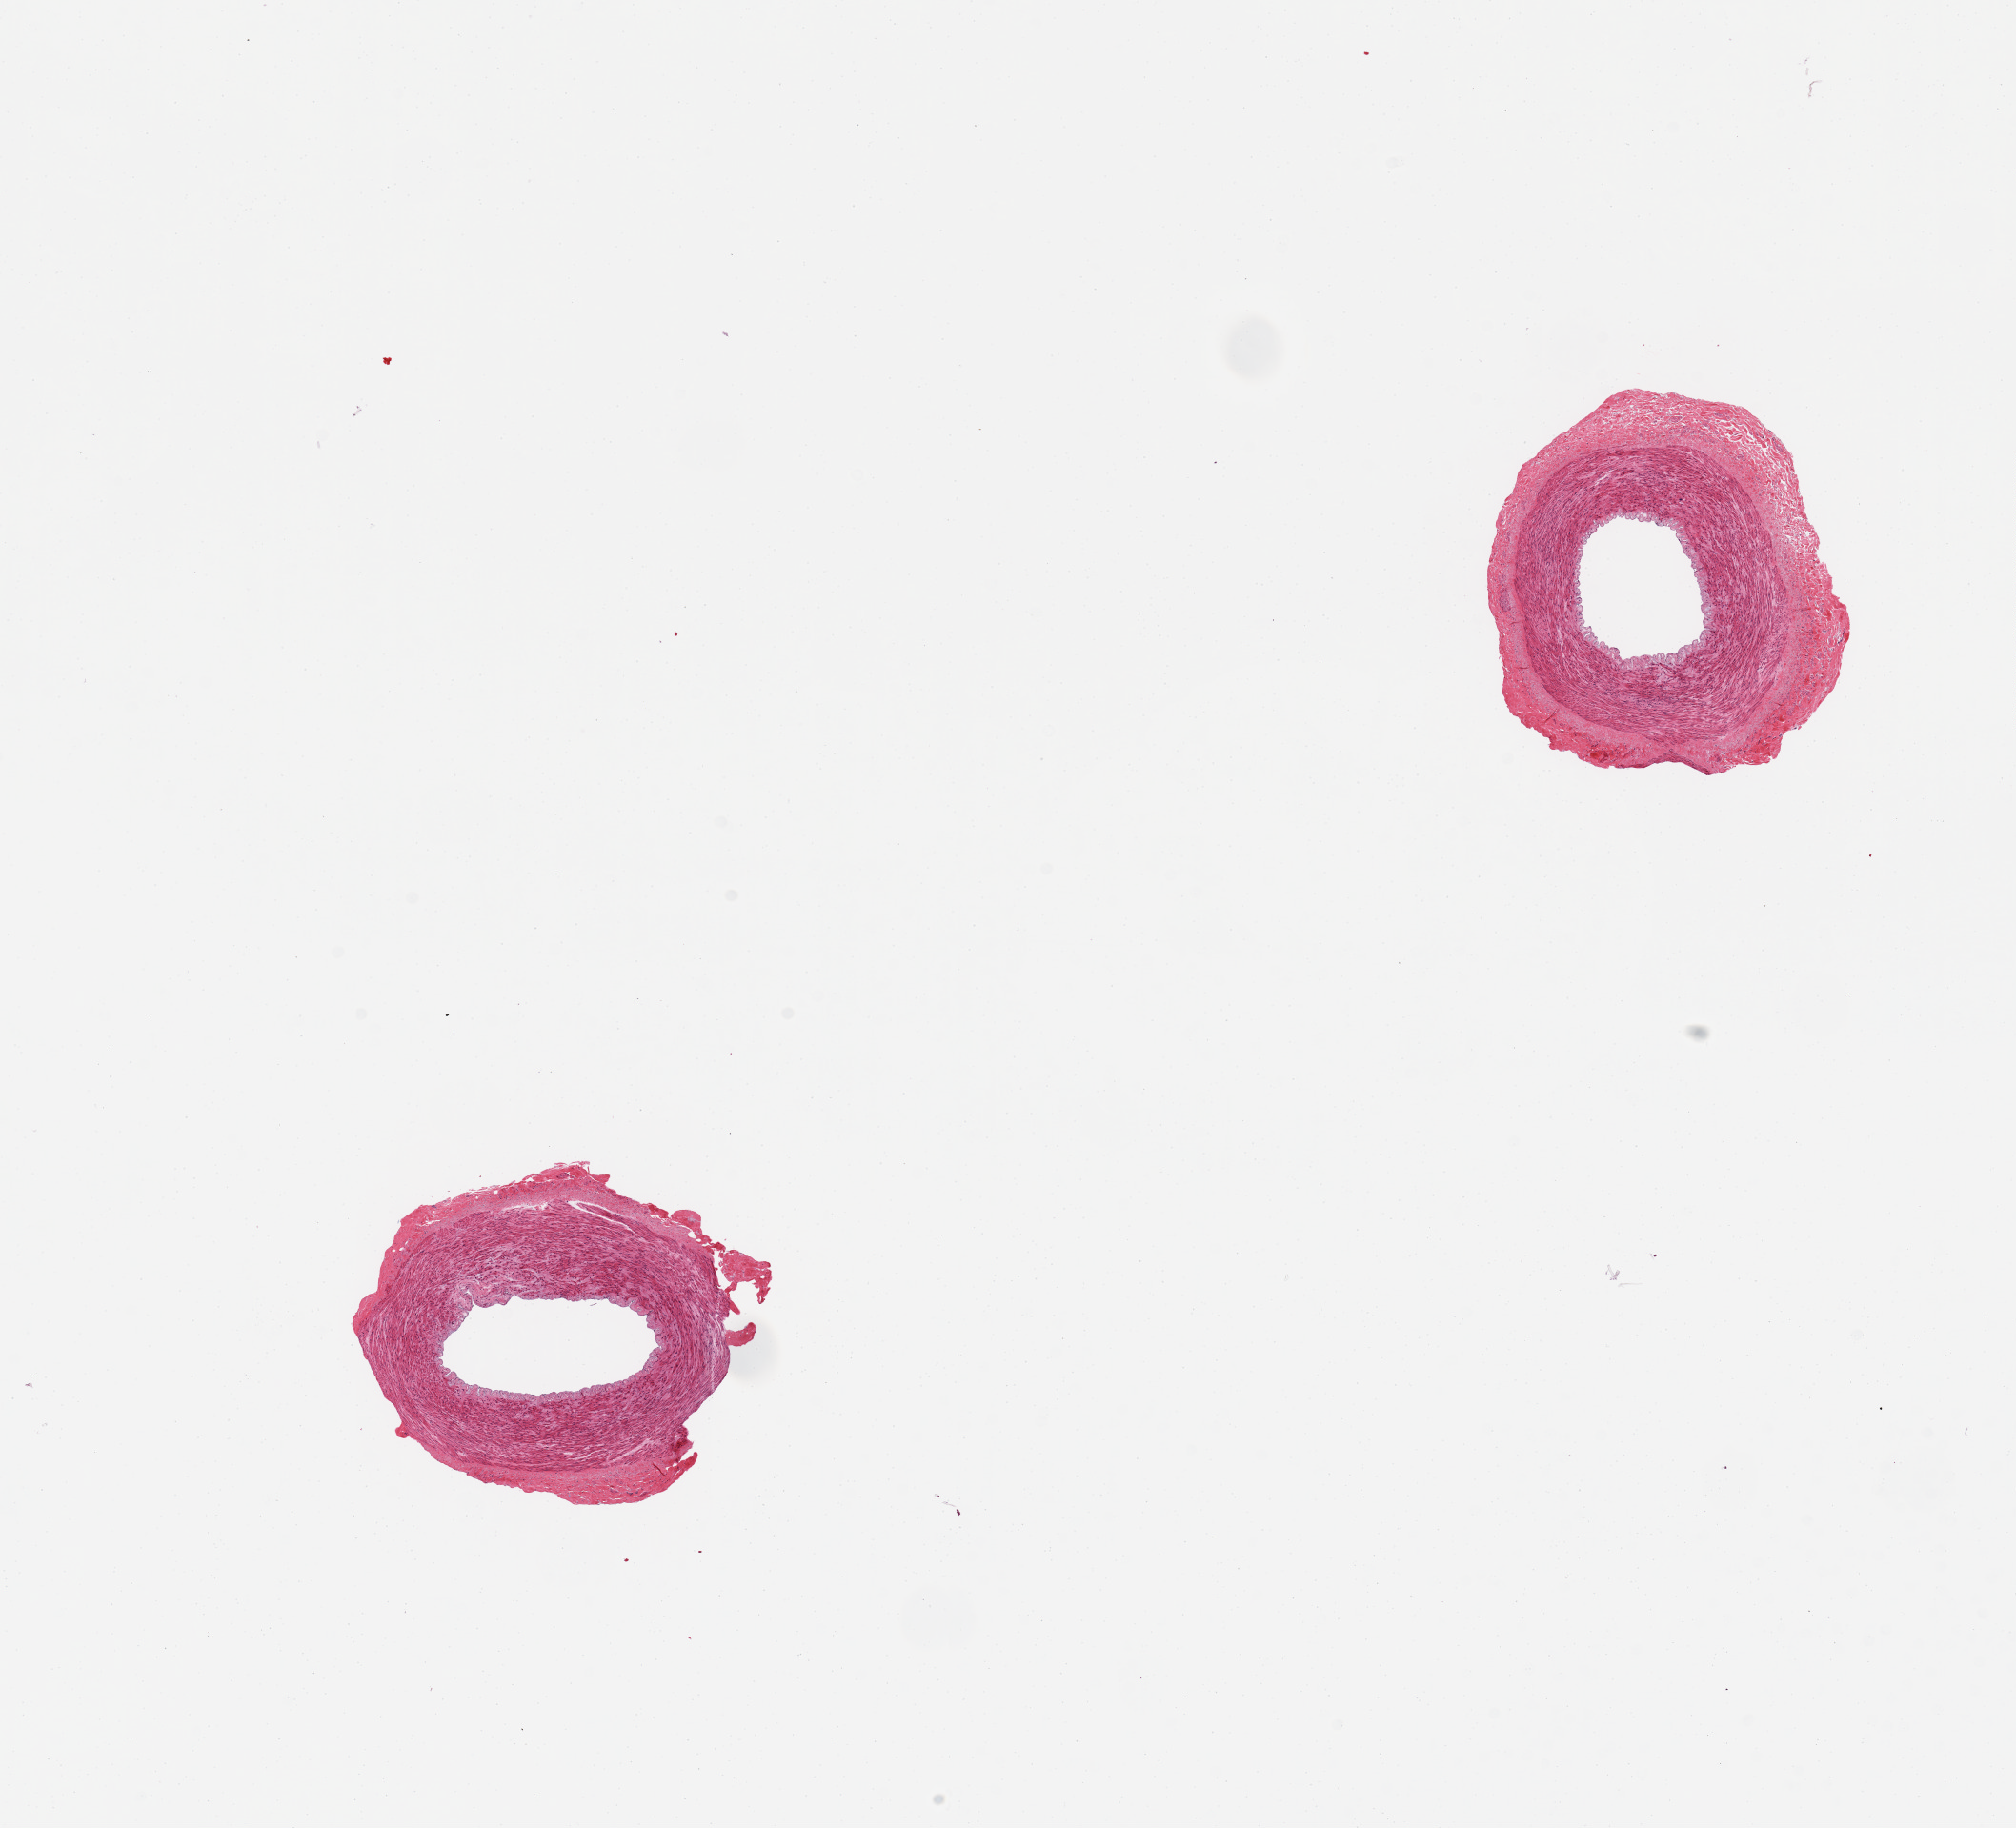
H&E whole-slide image, shown as a low-resolution overview of the whole scanned area (about 16.7 x 15.2 mm, from a 20x scan), PAXgene-fixed, paraffin-embedded tissue, target tissue: tibial artery, donor tissue sample. Female donor.
Reviewer comment on this tissue sample: 2 pieces; no lesions.